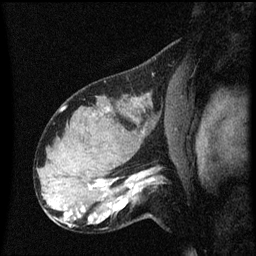
Breast MRI (dynamic contrast-enhanced), one sagittal slice. Slice 38 of 60 in the series (ordered by position). Dynamic contrast-enhanced series, image 2 of 3 at this slice position (ordered by acquisition). 1.5 T. TE 4.2 ms, TR 8.4 ms. 2 mm slice thickness. 256 × 256 image matrix, field of view 200 × 200 mm. Patient: female, 31 years. From the clinical record (not read from this slice): setting: breast cancer imaged before/during neoadjuvant chemotherapy; receptor status: HR-positive, HER2-negative.
Structures marked on this image (semi-automatic segmentation, software-assisted and operator-edited):
- analysis volume of interest (the breast-tissue region the enhancement analysis was run in; not a lesion): bounding box (x1, y1, x2, y2) in pixels: (102, 166, 169, 223)
- tumour enhancement mask (voxels above the 70 % enhancement threshold inside the analysis volume of interest): (104, 172, 150, 221)